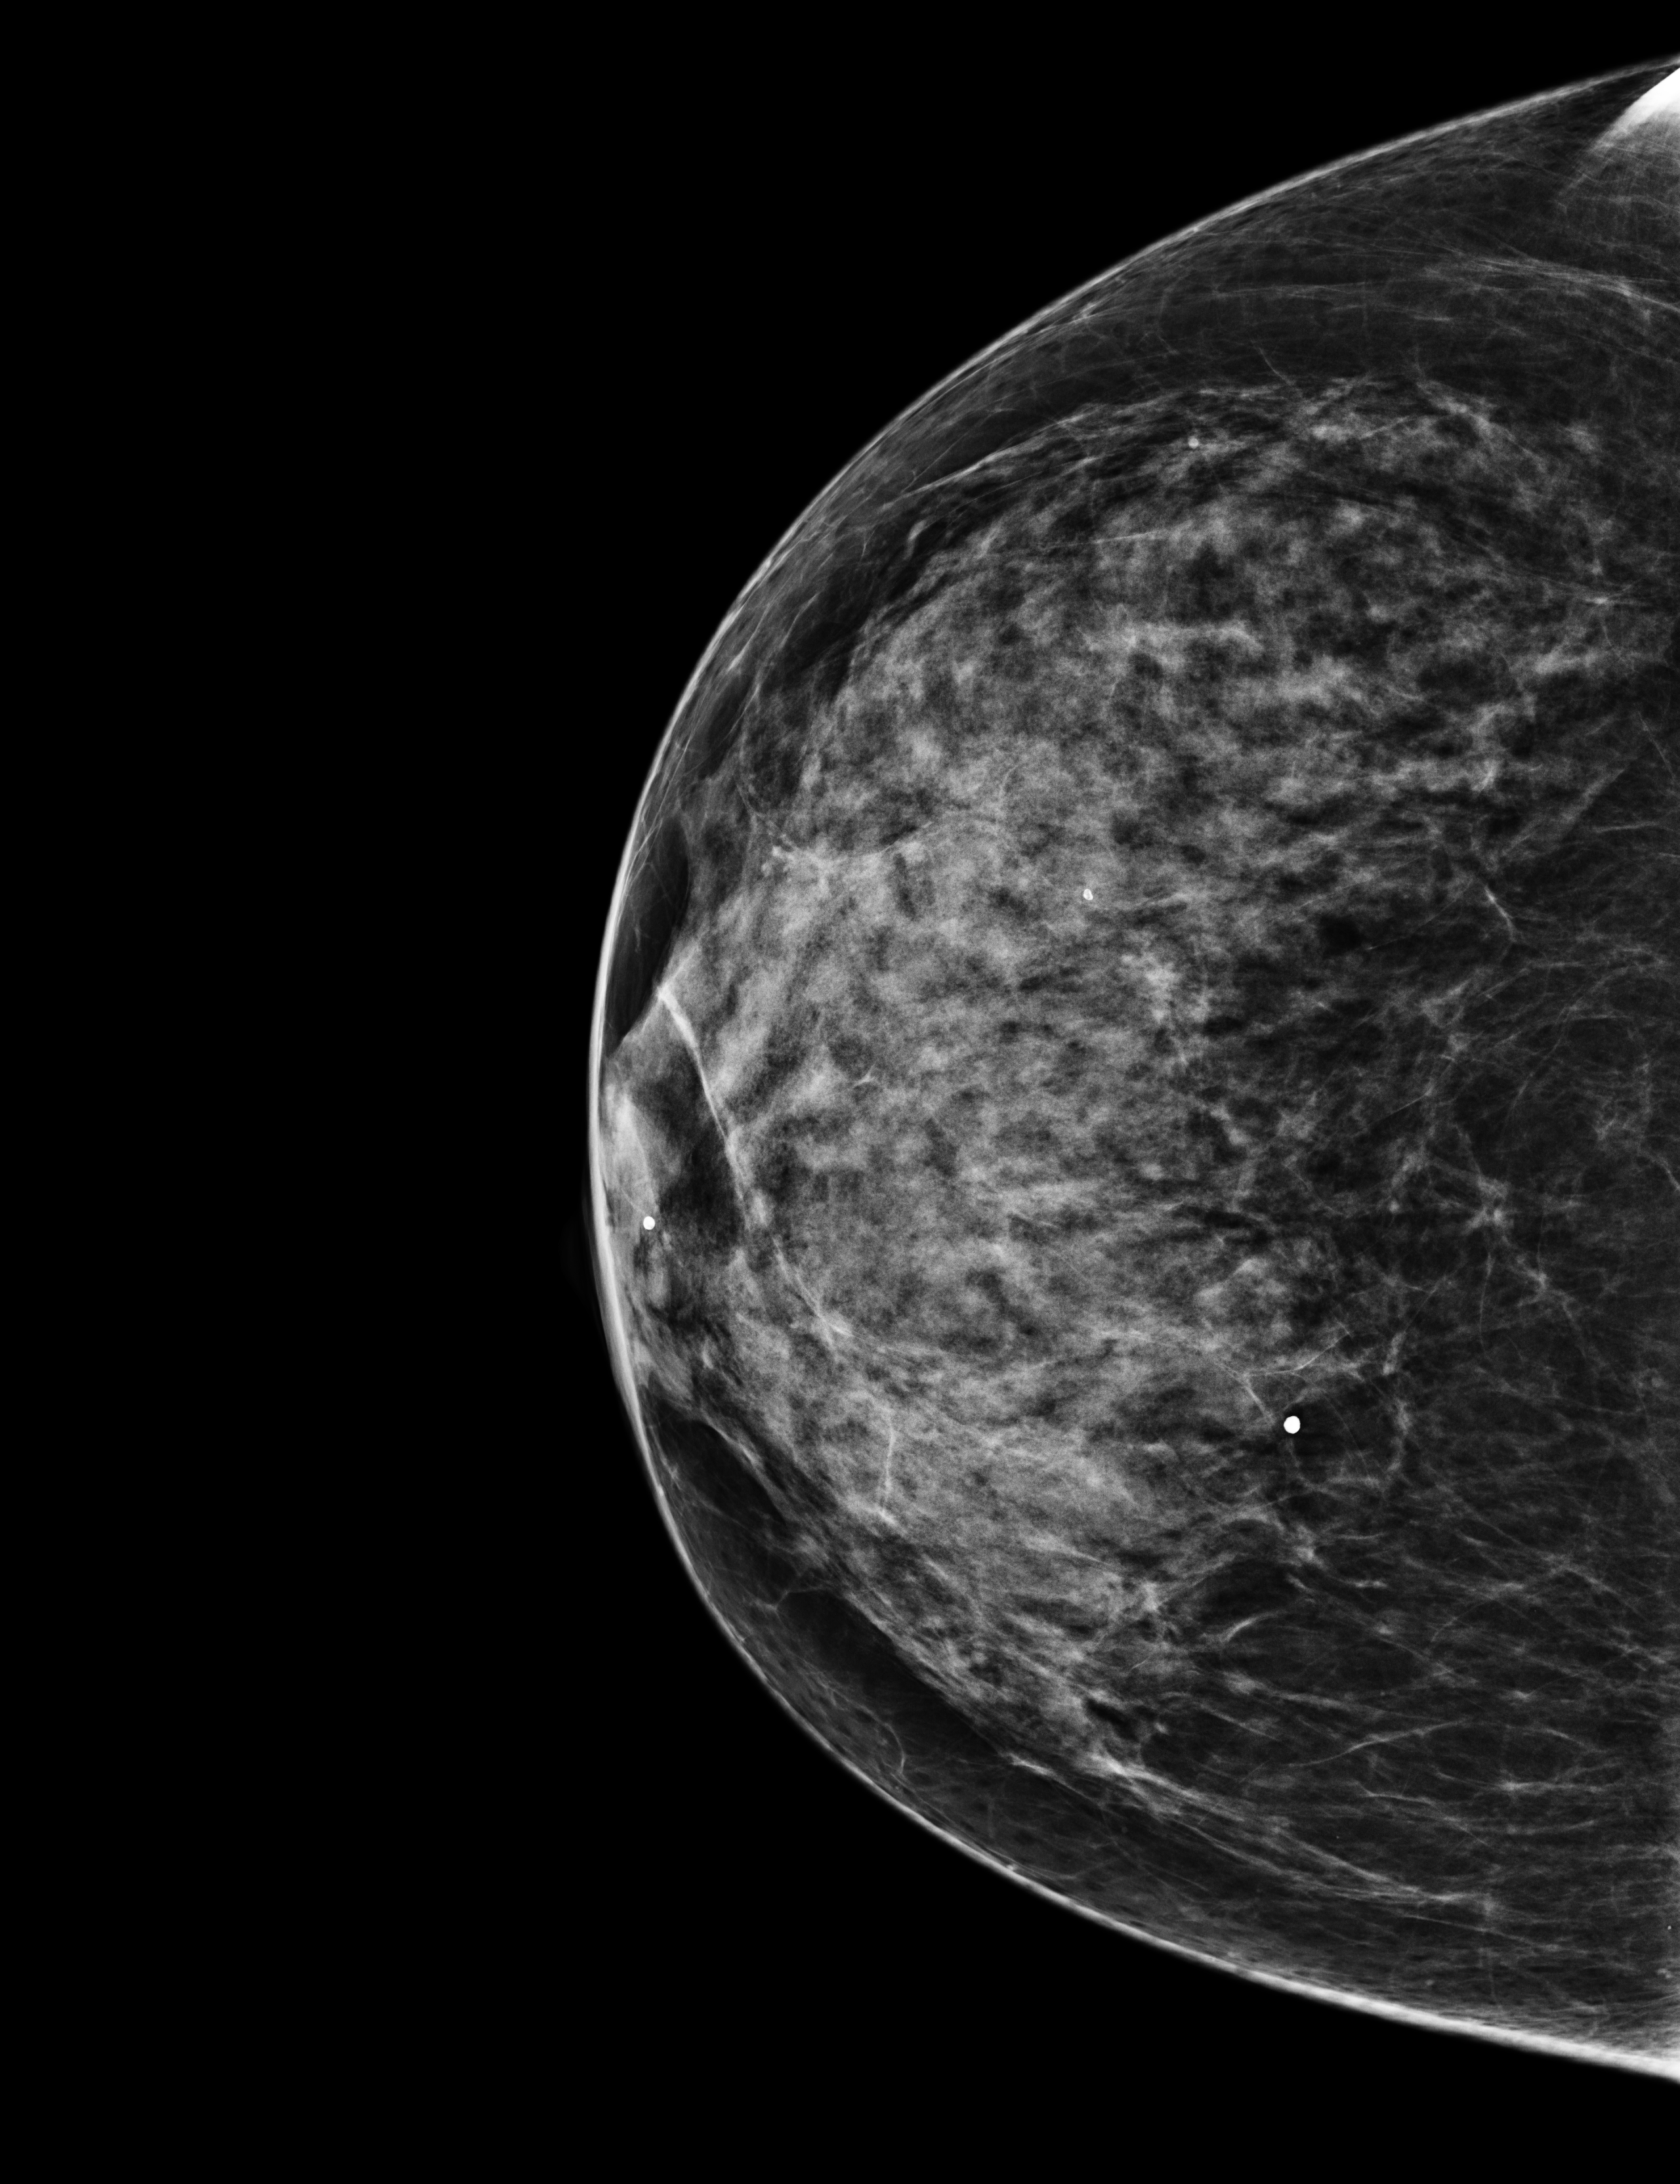
Digital mammogram (FFDM), right breast, craniocaudal (CC) view, annual screening mammography examination, compressed breast thickness 72 mm. Patient aged 58 years (female).
- BI-RADS breast density category at the screening exam (both breasts, scale 1–4): 3
- final BI-RADS category for the screening round (tomosynthesis exam, both breasts): category 1
- recall: no recall after this screen